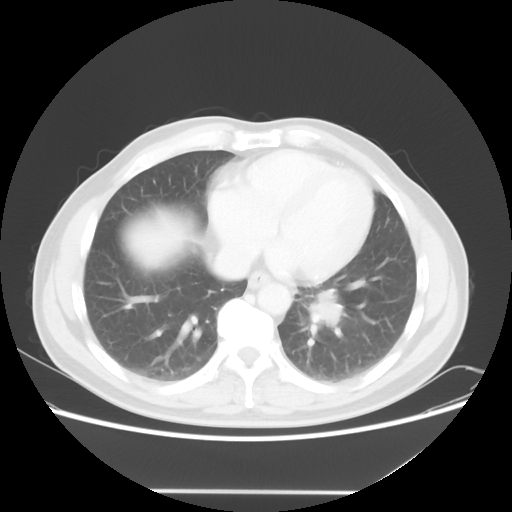
Chest CT, one axial slice; slice 19 of 56 in the series (ordered by position); 120 kVp; lung window (W 1500 / L -600 HU); 512 × 512 image matrix, field of view 385 × 385 mm. Patient: male, 61 years. From the clinical record (not read from this slice): clinical TNM (as recorded): T1c N0 M0.
Structures marked on this image (bounding box drawn by a radiologist):
- lung tumour (recorded histology: adenocarcinoma): bounding box [x1, y1, x2, y2] px = [302, 280, 352, 331]